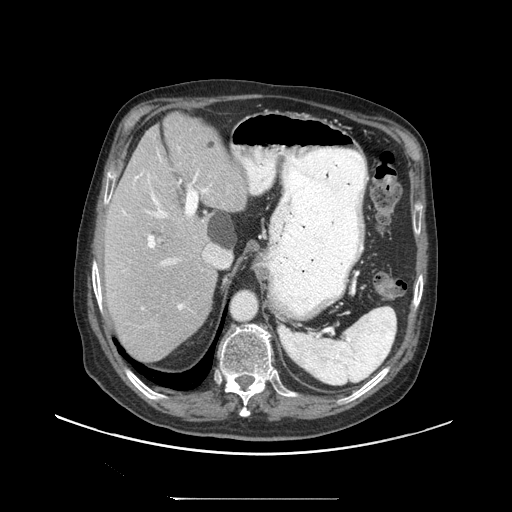
Contrast-enhanced abdominal CT (liver protocol), one axial slice; position 69 of 97 along the scan axis; reconstruction kernel STANDARD; 140 kVp; soft-tissue window (W 400 / L 40 HU); 2.5 mm slice thickness; 512 × 512 image matrix. From the clinical record (not read from this slice): diagnosis: hepatocellular carcinoma (patient treated with transarterial chemoembolisation; whether this scan precedes or follows treatment is not stated here); TNM stage (as recorded): Stage-IIIC.
Annotated regions visible in this slice (semi-automatically segmented with operator editing):
- abdominal aorta: box from (x=232, y=292) to (x=256, y=320) px
- liver parenchyma outside the tumour (the mass and vessels are separate outlines, so this box may not span the whole liver): (x=104, y=112)–(x=248, y=360)
- liver vessels: (x=122, y=153)–(x=210, y=310)